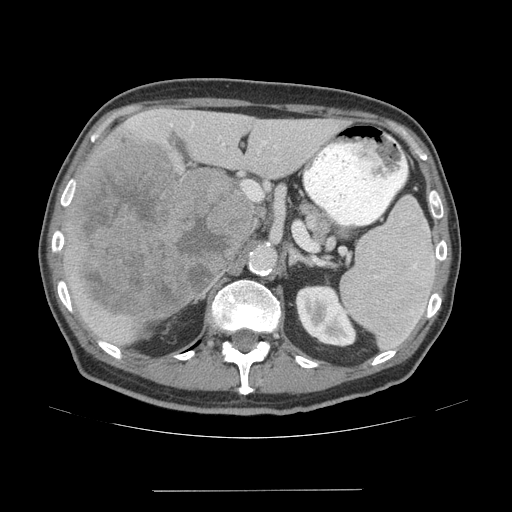
Contrast-enhanced abdominal CT (liver protocol), one axial slice. Slice 33 of 77 in the series (ordered by position). 140 kVp. Soft-tissue window (W 400 / L 40 HU). 512 × 512 image matrix. Case-level facts recorded for this patient, not image findings: diagnosis: hepatocellular carcinoma (patient treated with transarterial chemoembolisation; whether this scan precedes or follows treatment is not stated here); TNM stage (as recorded): Stage-IVA; Child-Pugh class: A; tumour nodularity: uninodular.
Annotated regions visible in this slice (semi-automatically segmented with operator editing):
- liver parenchyma outside the tumour (the mass and vessels are separate outlines, so this box may not span the whole liver): box from (x=64, y=108) to (x=349, y=346) px
- mass: (x=67, y=138)–(x=255, y=318)
- liver vessels: (x=170, y=122)–(x=275, y=201)